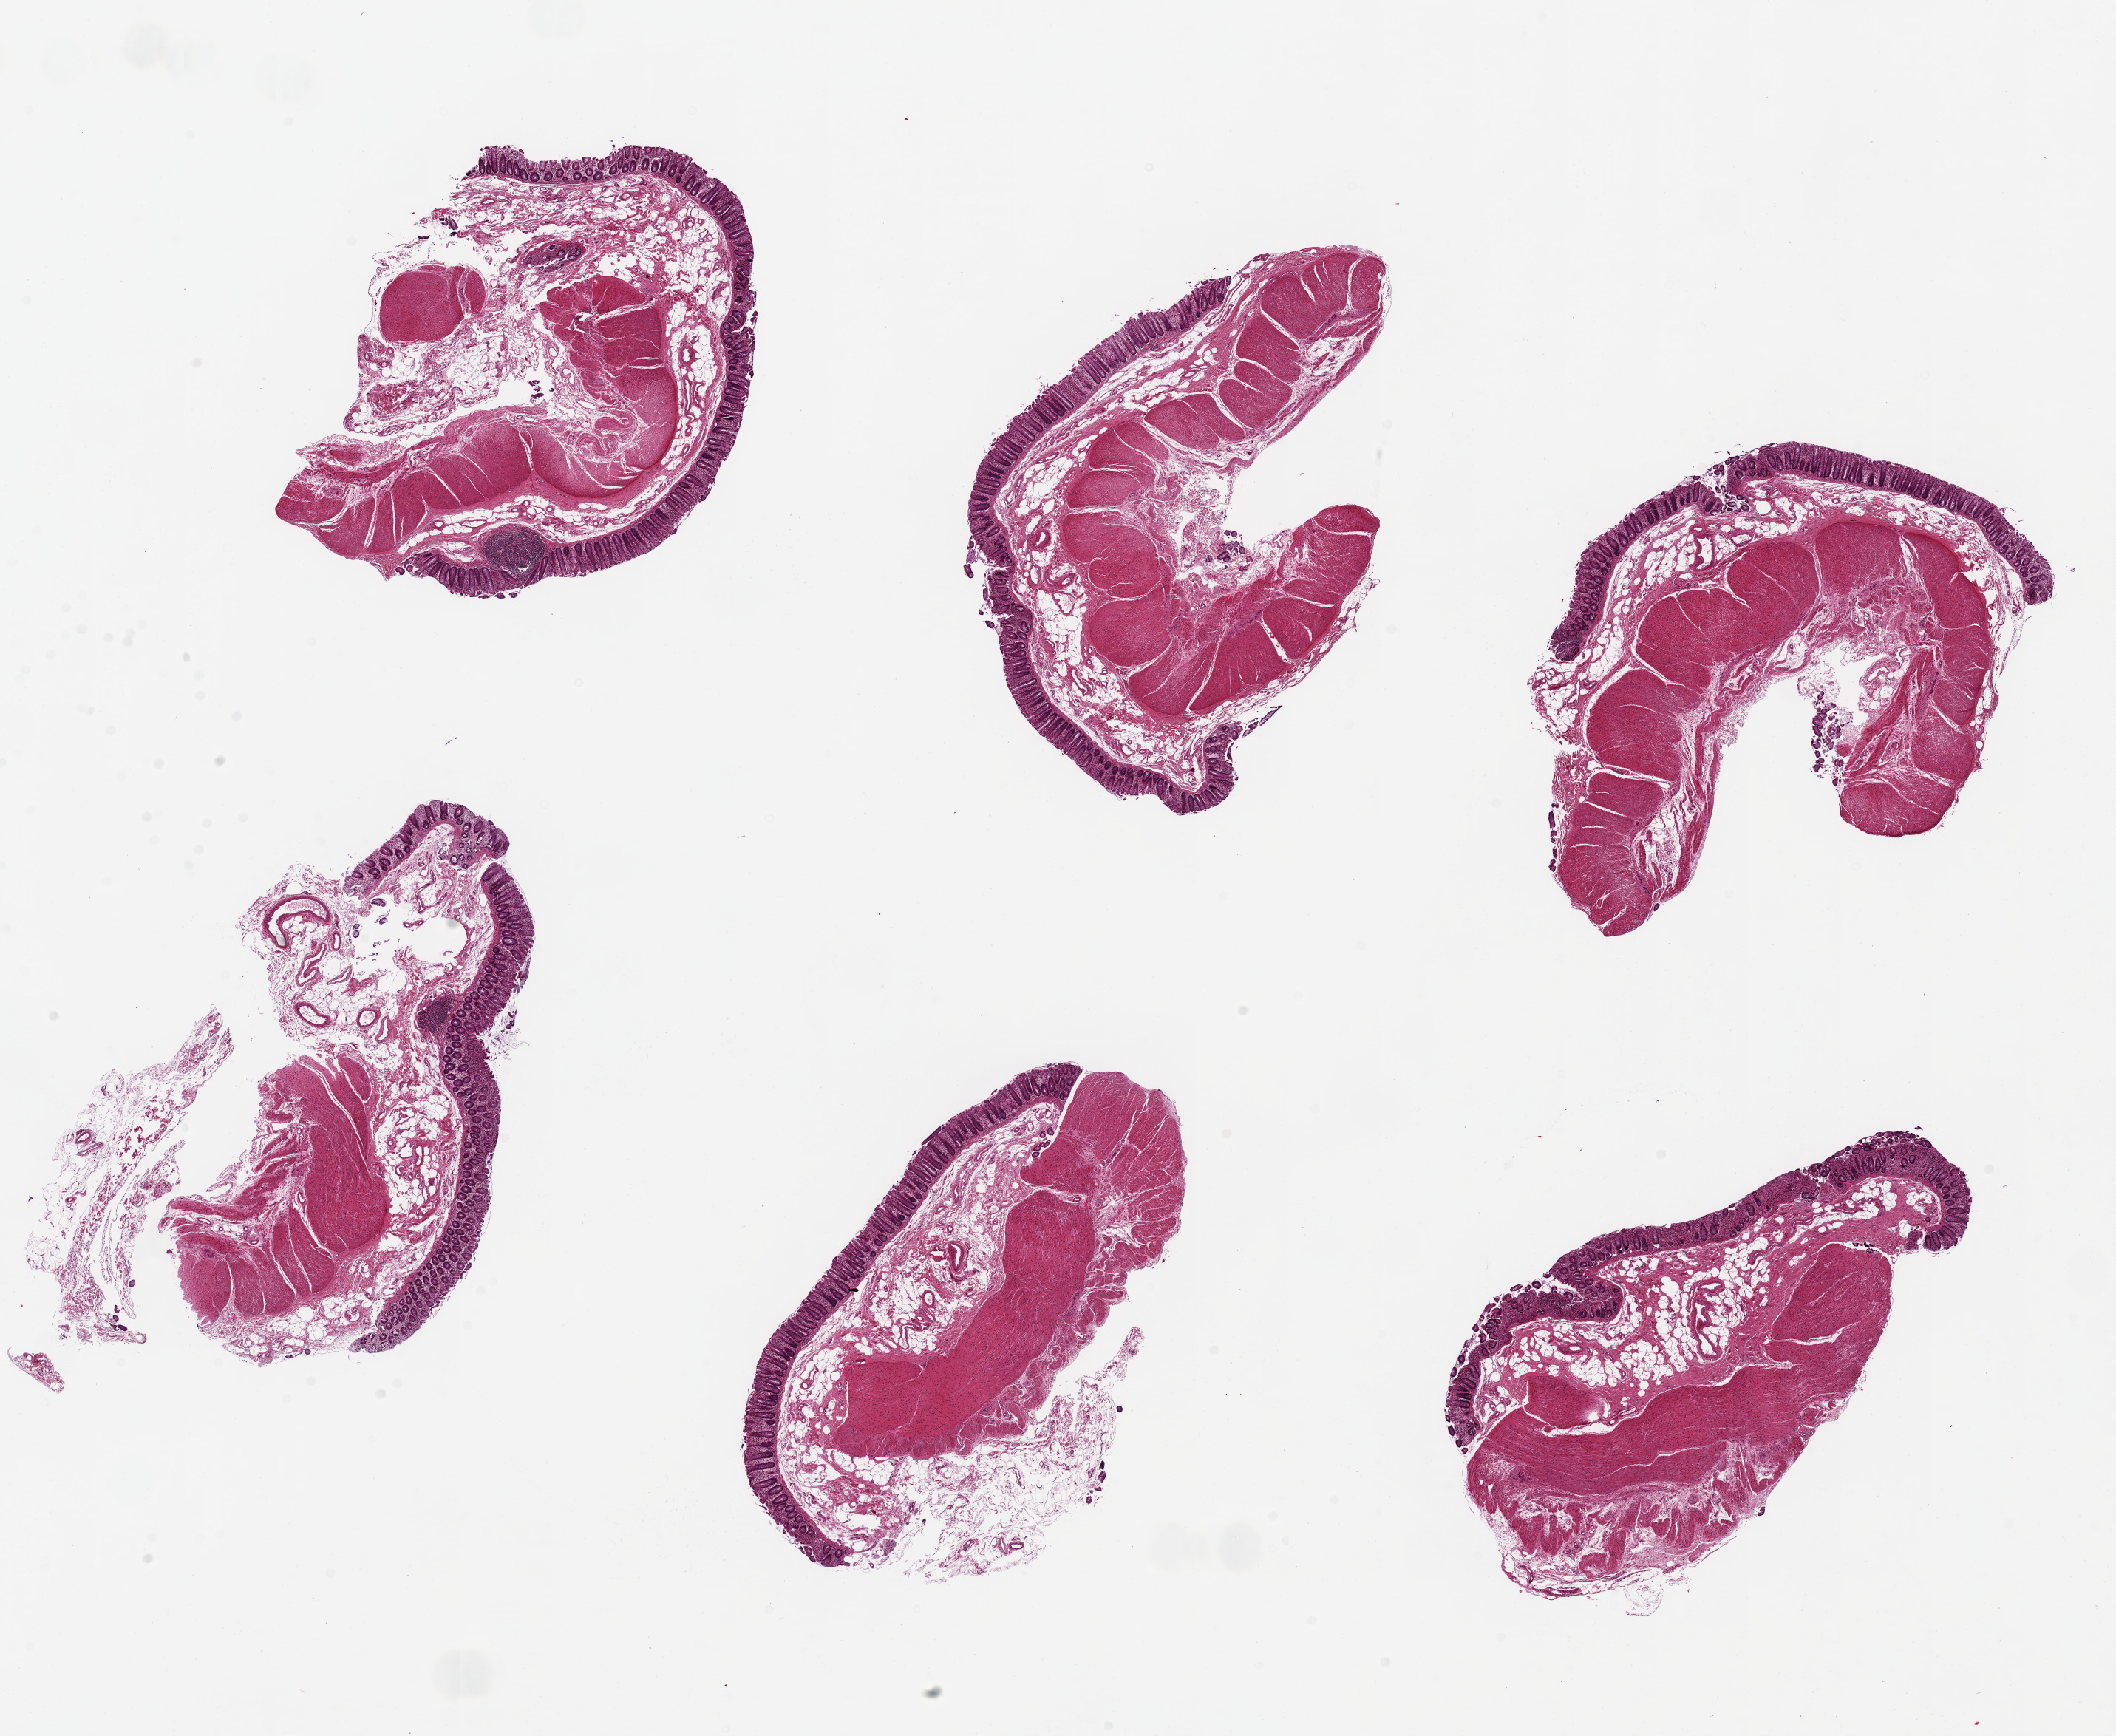
Digitized H&E-stained section, whole scanned area (about 22.6 x 18.6 mm) shown as a low-resolution overview. PAXgene-fixed paraffin-embedded (PFPE) section. Section of transverse colon (target tissue). Donor tissue sample.
Pathologist's review note for this sample: 6 pieces, up to 7.5x4mm; focally sloughed glands.